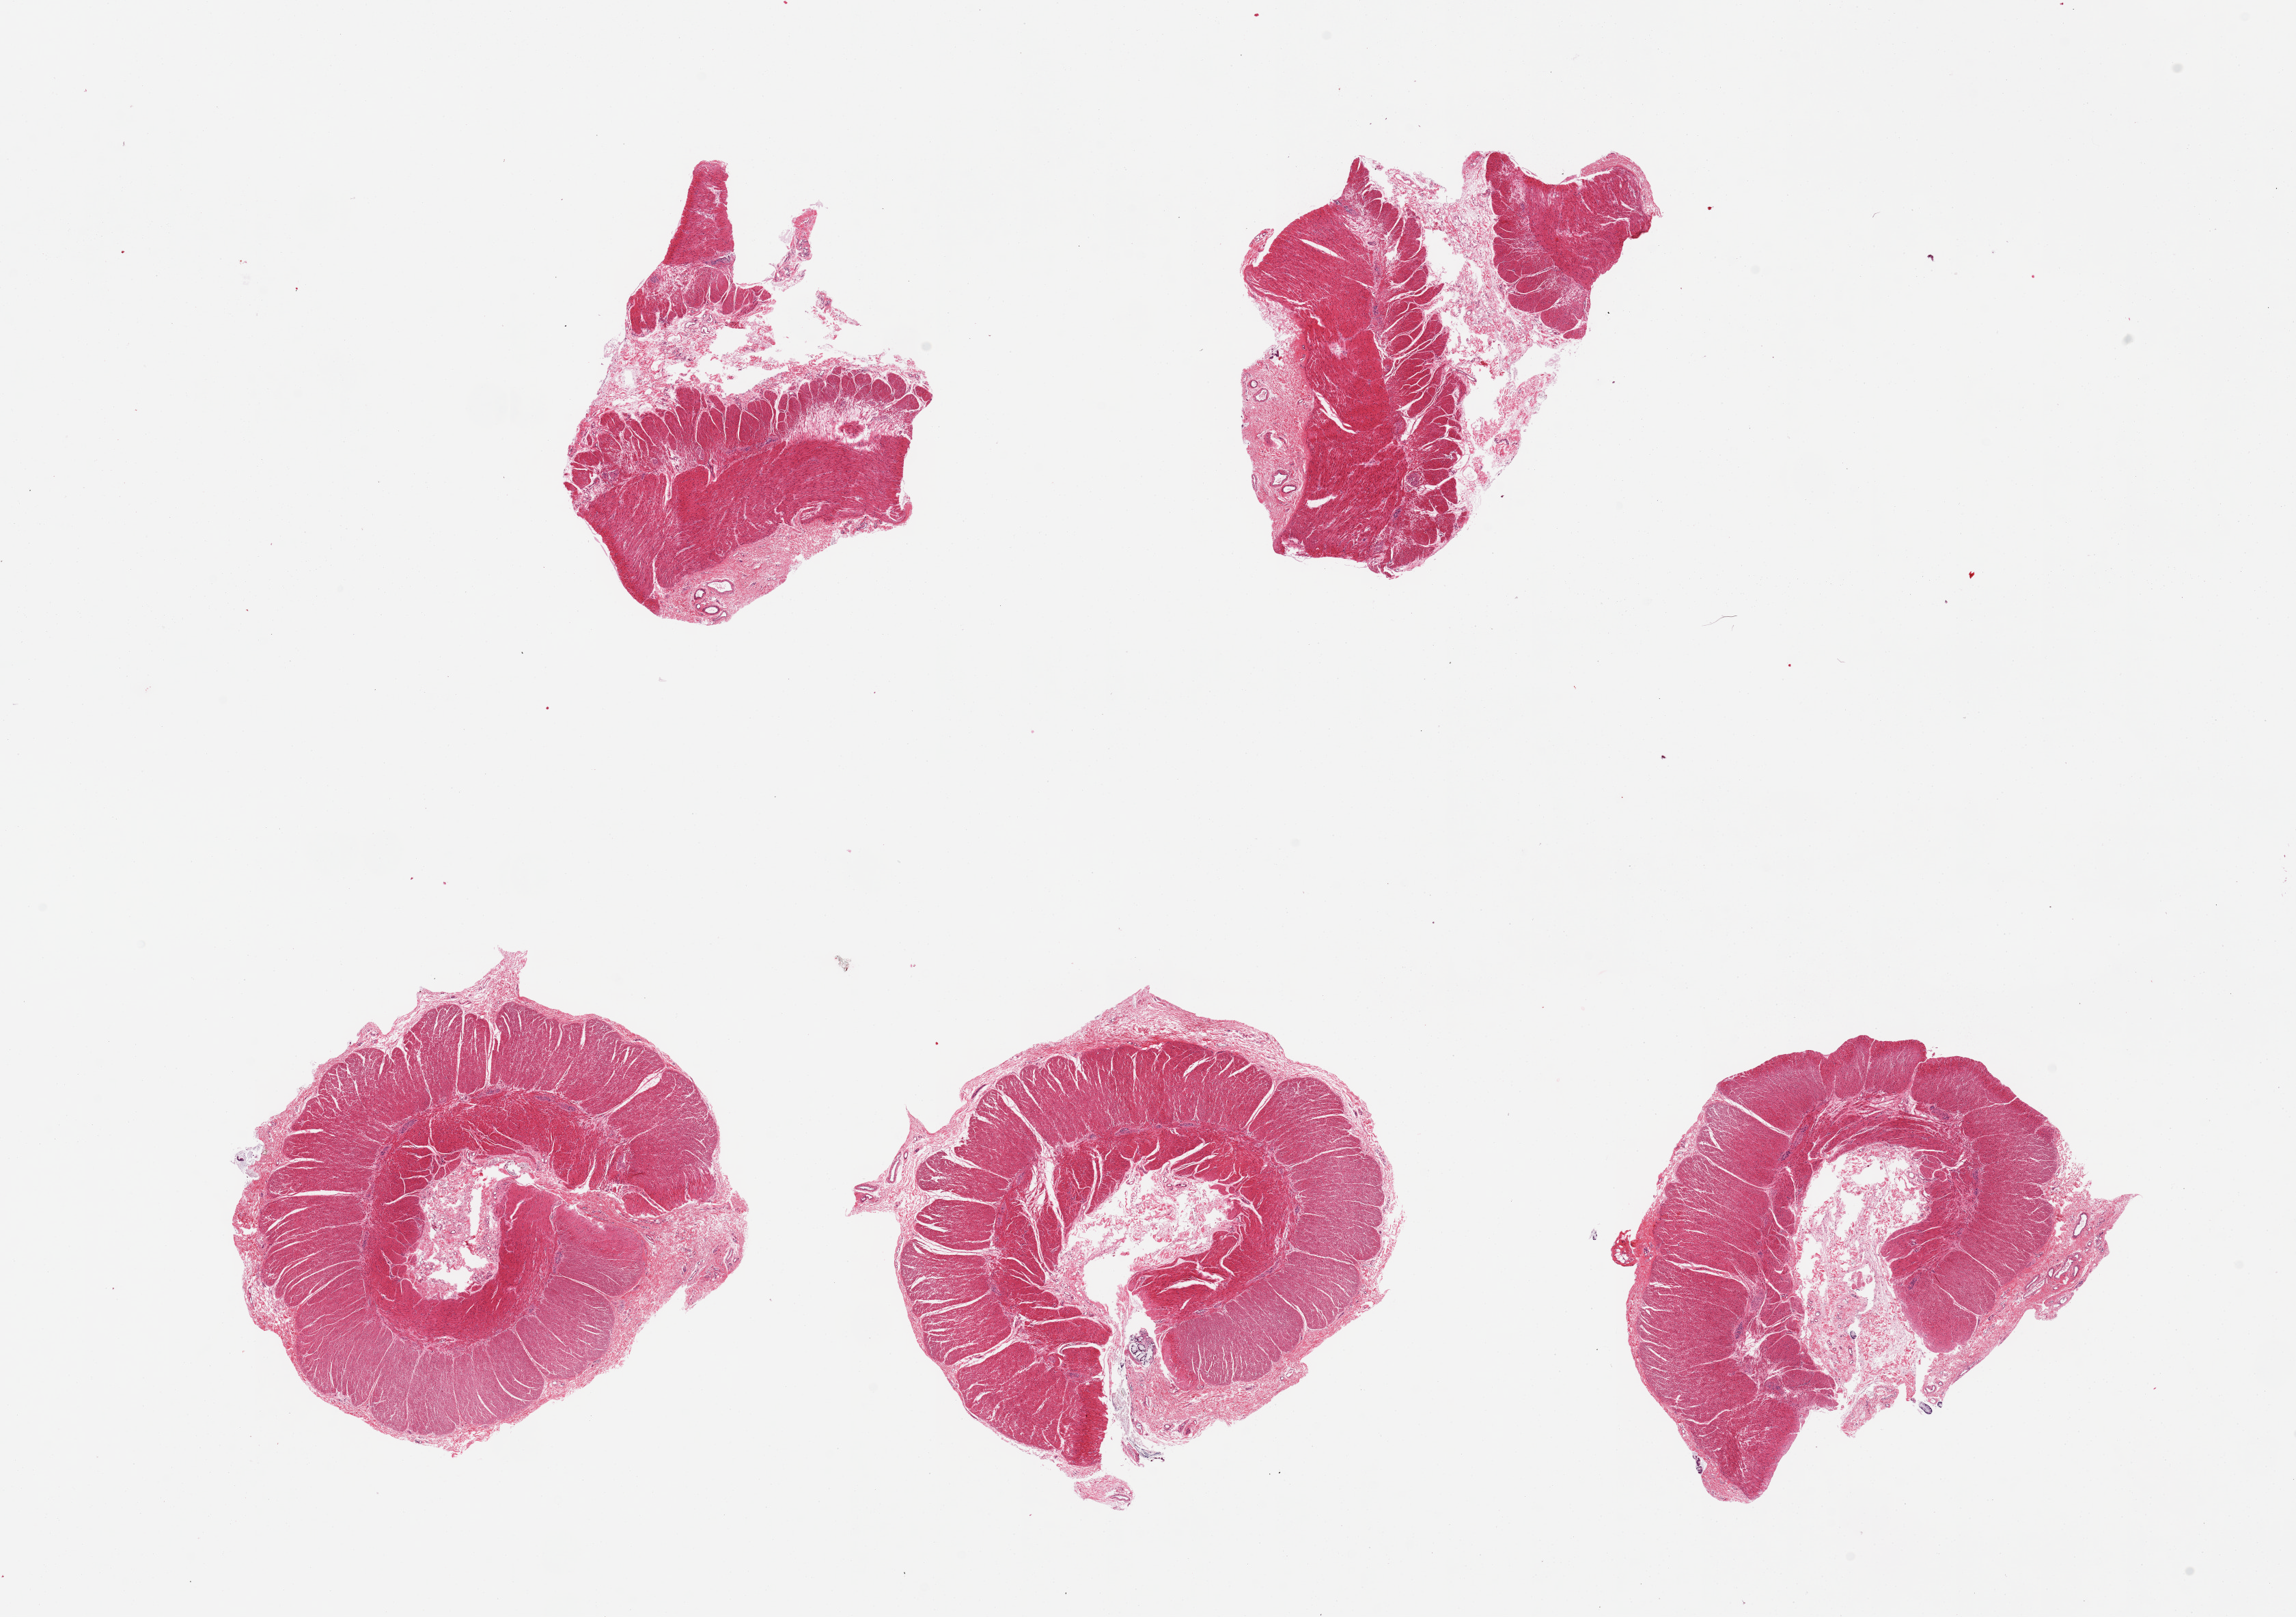
Digitized hematoxylin and eosin (H&E)-stained section, whole scanned area (about 26.6 x 18.7 mm) shown as a low-resolution overview; PAXgene-fixed paraffin-embedded (PFPE) section; sampled site (target tissue): sigmoid colon; tissue donor sample.
Reviewer comment on this tissue sample: 5 pieces.